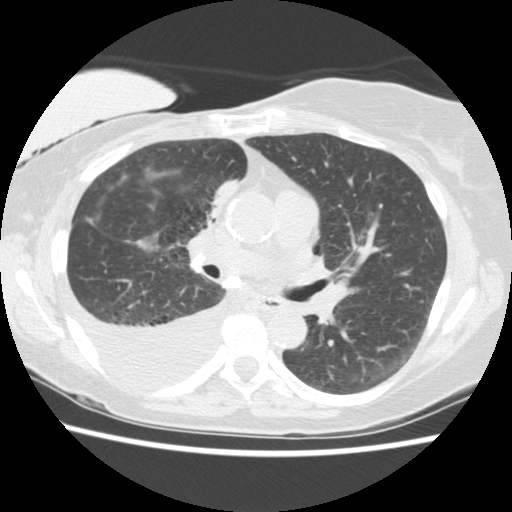
Low-dose screening chest CT, one axial slice; position 85 of 157 along the scan axis; reconstruction kernel STANDARD; 120 kVp; lung window (W 1500 / L -600 HU); 2.5 mm slice thickness; 512 × 512 image matrix.
Outlined on this slice (manually delineated by an expert):
- lesion 1 (tumor, upper lobe of right lung): box from (x=212, y=180) to (x=240, y=217) px